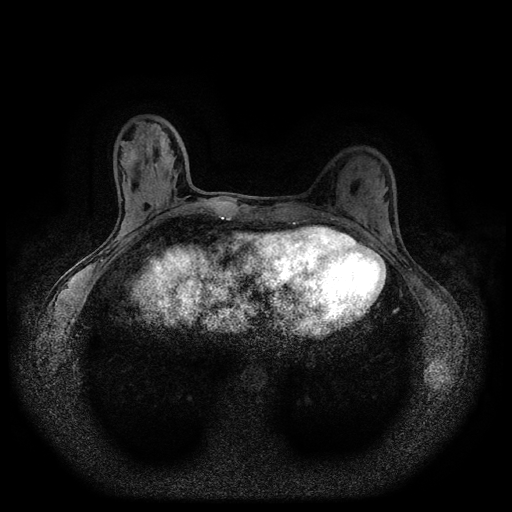
Breast MRI (dynamic contrast-enhanced, multi-phase), one axial slice. Dynamic contrast-enhanced series, time point 2 of 5 at this slice position (early post-contrast). 1.5 T. TE 2.7 ms, TR 5.4 ms. 512 × 512 image matrix. Patient: female, 32 years.
Outlined on this slice (semi-automatically segmented with operator editing):
- breast lesion (labelled benign in the annotation): box from (x=125, y=147) to (x=139, y=164) px